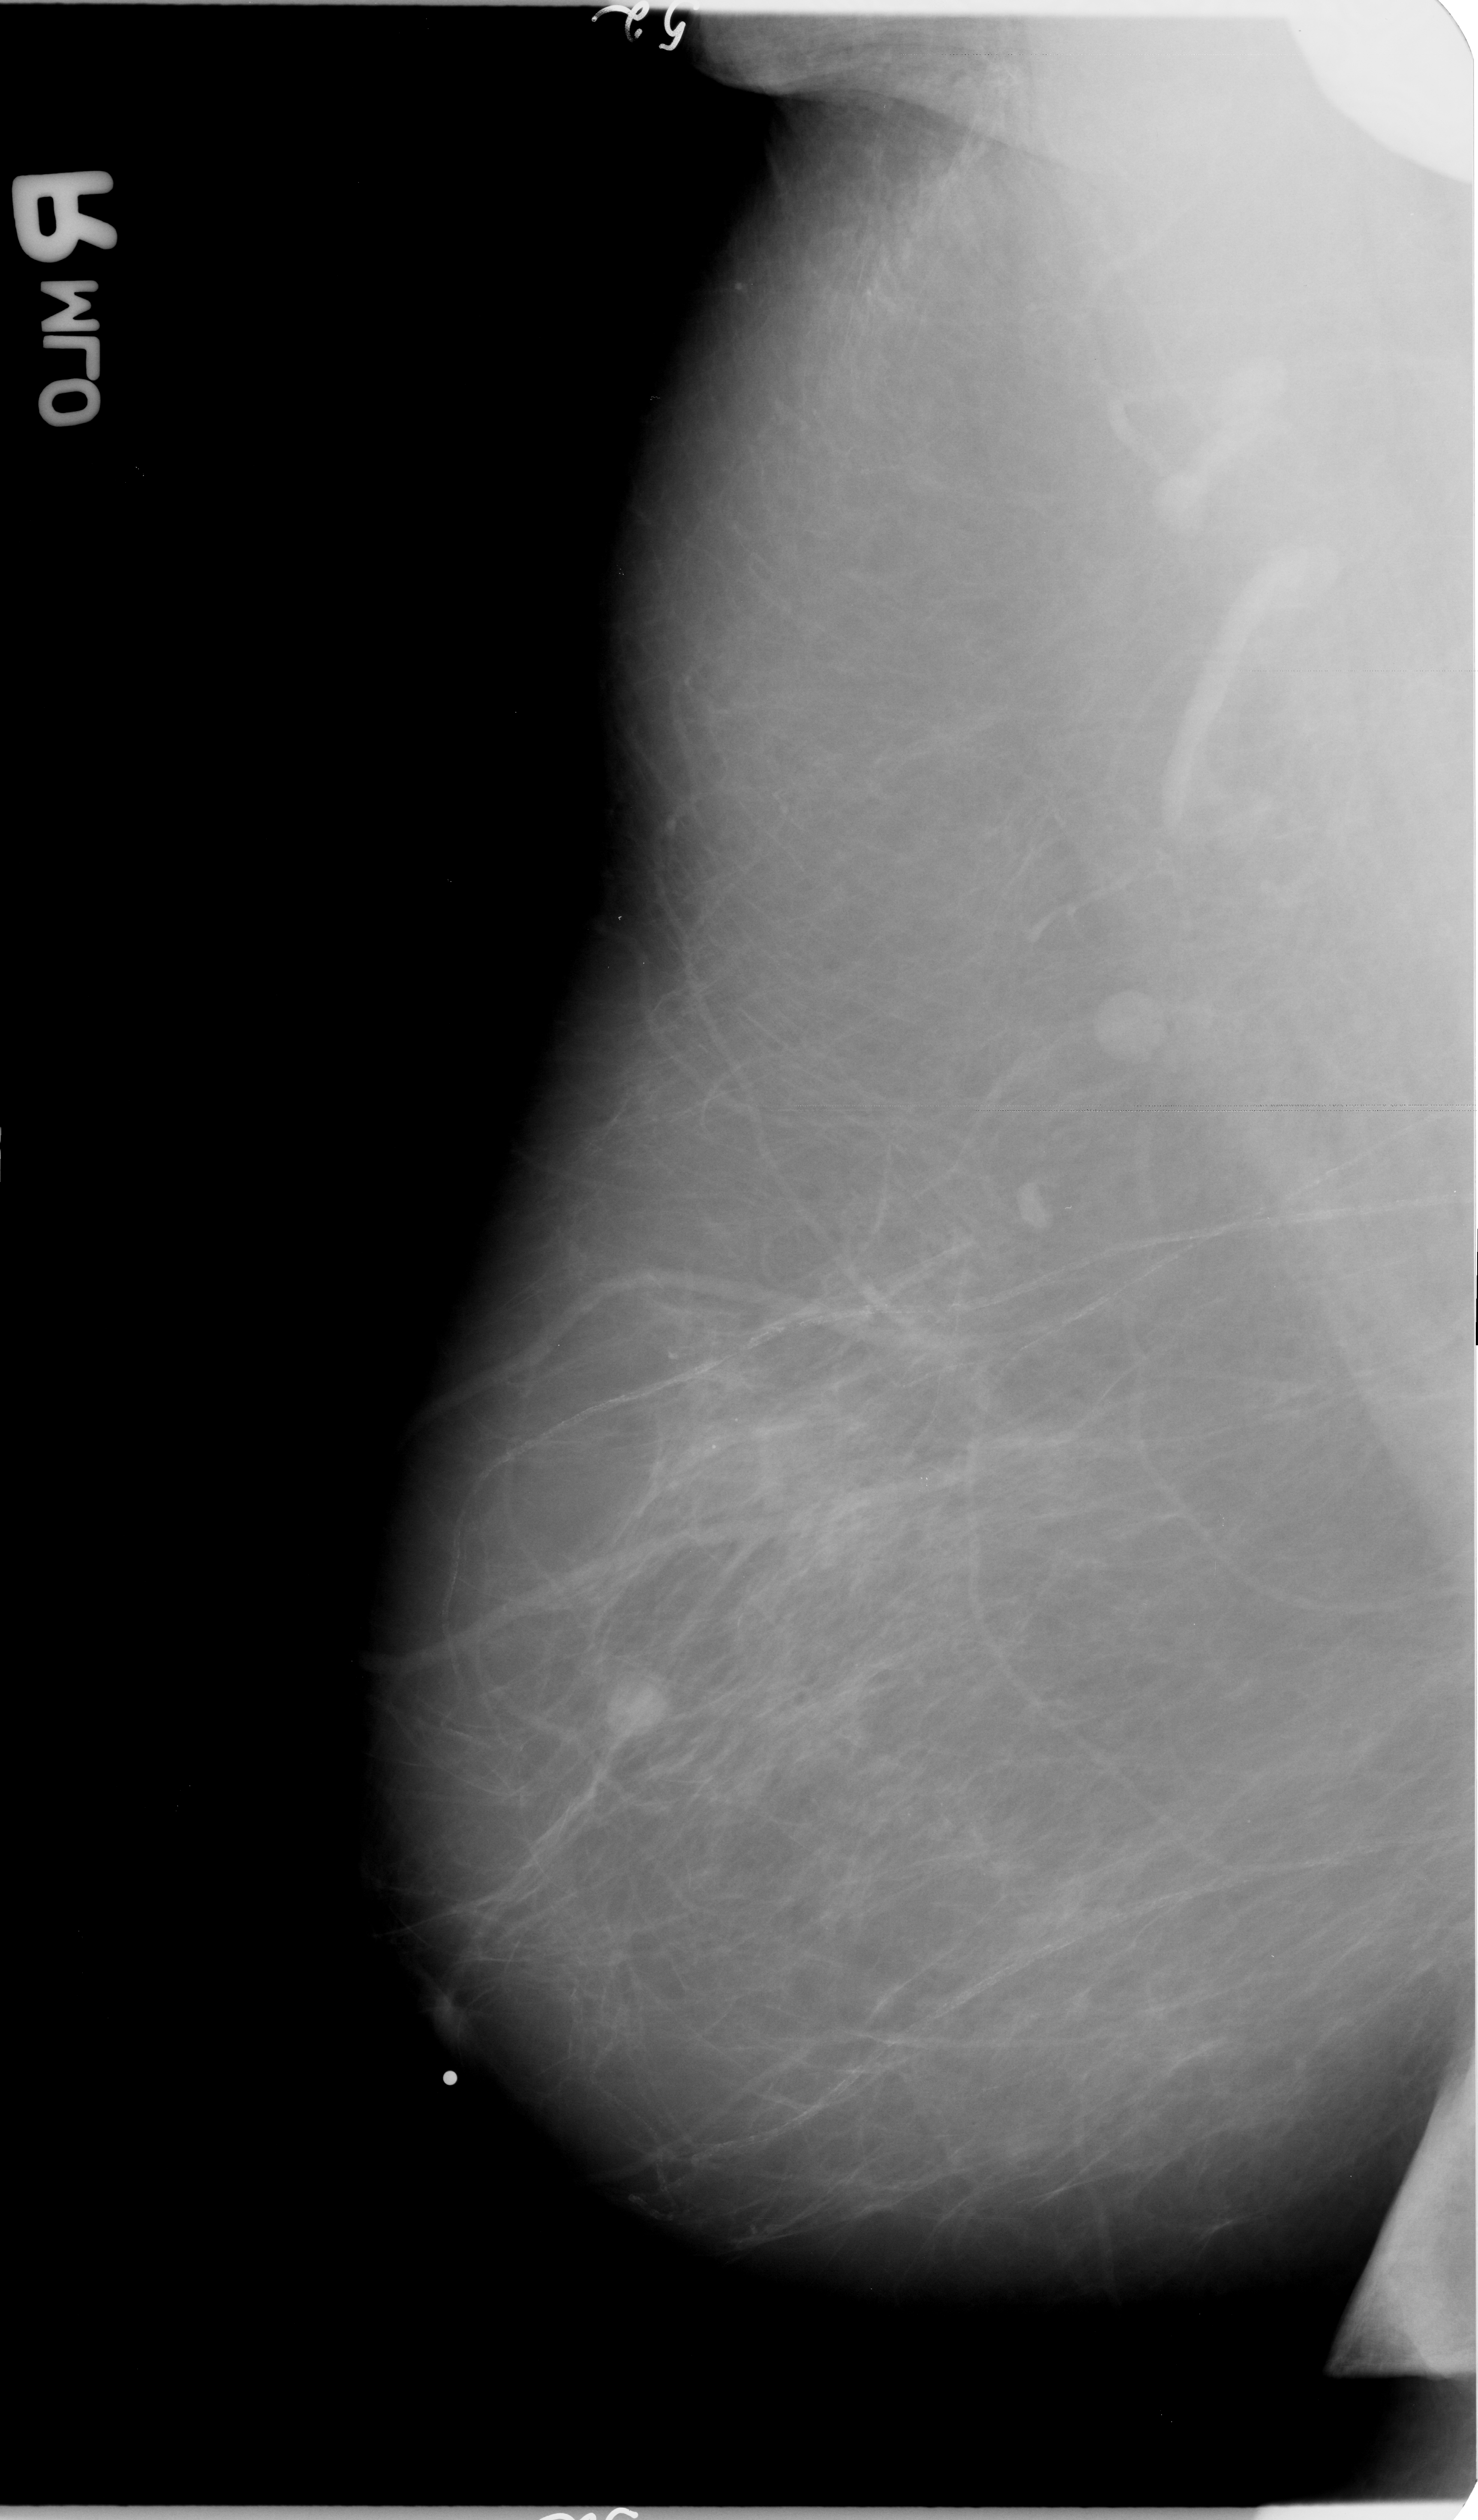
Scanned film-screen mammogram, right breast, mediolateral oblique (MLO) view, breast composition: almost entirely fatty (BI-RADS density category 1 of 4).
Finding: mass, shape irregular, margins ill defined; BI-RADS assessment category 3; subtlety rating 2 on a 1 (subtle) to 5 (obvious) scale; pathology (as recorded): malignant.